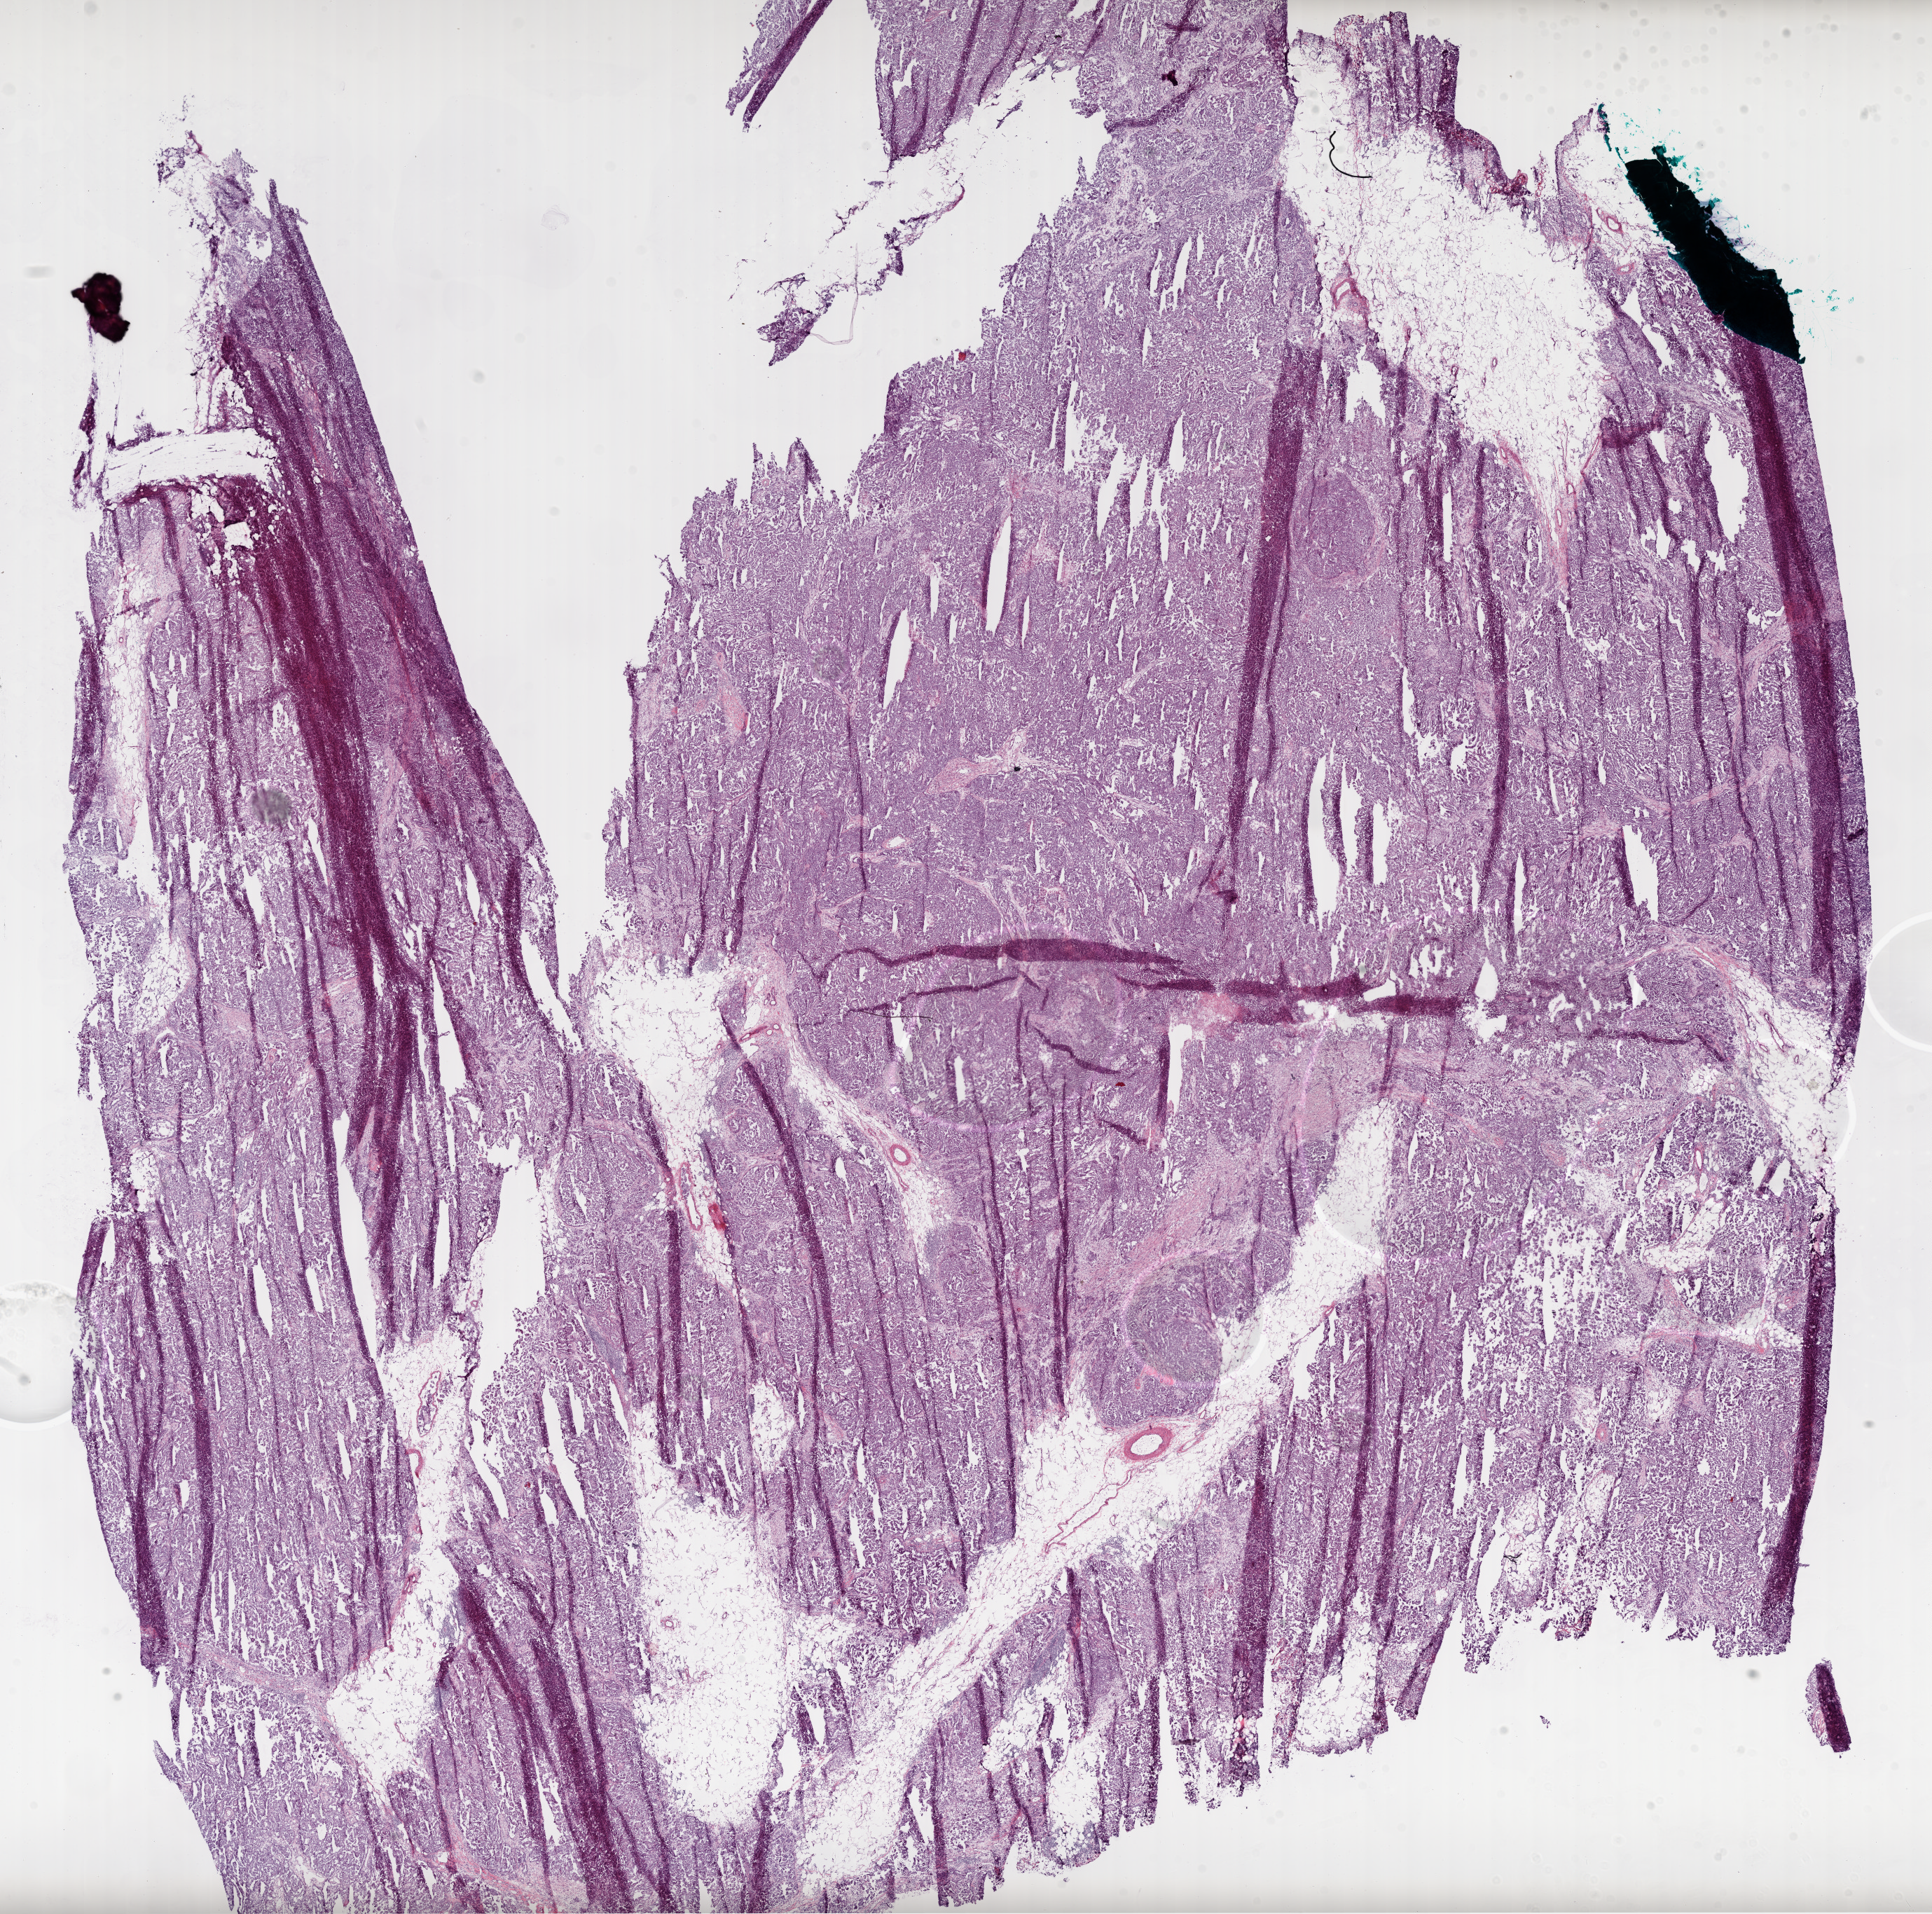
Hematoxylin and eosin (H&E) stained whole-slide image — shown as a low-resolution overview of the whole scanned area (about 22.2 x 22.0 mm), frozen section, primary tumour sample from the ovary. Female patient; age at initial diagnosis 42 years. Histologic grade: G3 (poorly differentiated). Pathologist review of this section (percent, as recorded): tumour cells 95%, tumour nuclei 98%, normal cells 0%, stromal cells 5%, necrosis 0%.
Pathologic diagnosis: Serous cystadenocarcinoma, NOS. FIGO stage: IV.